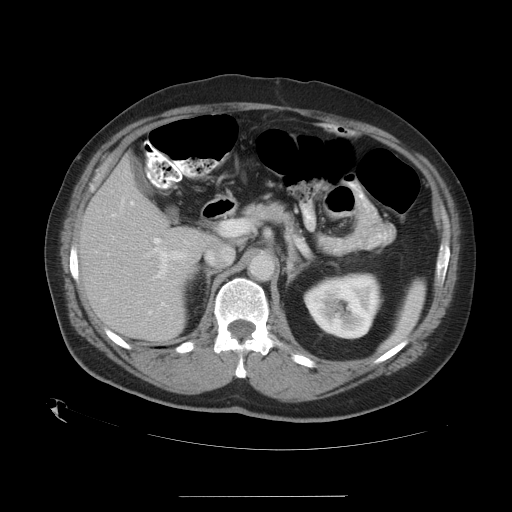
Contrast-enhanced abdominal CT, one axial slice; slice 18 of 35 in the series (ordered by position); 120 kVp; intravenous contrast given; soft-tissue window (W 400 / L 40 HU); 512 × 512 image matrix, field of view 450 × 450 mm. Male patient, age 67 years. From the clinical record (not read from this slice): diagnosis: colorectal cancer liver metastases, imaged before liver resection.
Outlined on this slice (manually delineated by an expert):
- hepatic veins: bounding box (x1, y1, x2, y2) in pixels: (130, 202, 151, 314)
- liver: (81, 159, 209, 339)
- planned liver remnant (the part of the liver to remain after resection): (81, 159, 209, 339)
- portal vein (with intrahepatic branches): (146, 221, 239, 280)